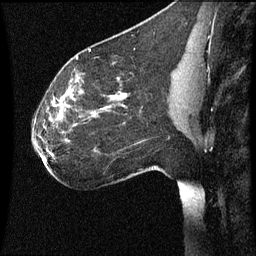
Breast MRI (dynamic contrast-enhanced), one sagittal slice; position 37 of 60 along the scan axis; dynamic contrast-enhanced series, image 2 of 3 at this slice position (ordered by acquisition); 1.5 T; TE 4.2 ms, TR 8.9 ms; 2 mm slice thickness; 256 × 256 image matrix. Female patient, age 35 years. Case-level facts recorded for this patient, not image findings: setting: breast cancer imaged before/during neoadjuvant chemotherapy; receptor status: HER2-positive.
Annotated regions visible in this slice (semi-automatic segmentation, software-assisted and operator-edited):
- analysis volume of interest (the breast-tissue region the enhancement analysis was run in; not a lesion): bounding box <30,66,177,177> (left, top, right, bottom; pixels)
- tumour enhancement mask (voxels above the 70 % enhancement threshold inside the analysis volume of interest): <65,94,126,109>